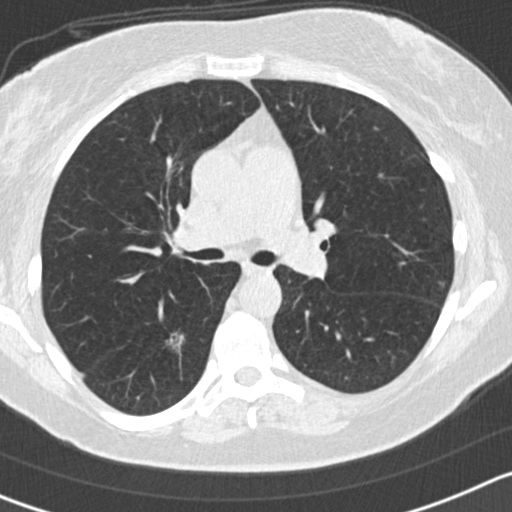
Low-dose screening chest CT, axial slice; baseline screening round; lung window (W 1500 / L -600 HU); 2 mm slice thickness; 512 × 512 image matrix. Female participant, aged 65 years at enrolment. Former smoker at enrolment.
• Expert-annotated lung lesion, bounding box [x1, y1, x2, y2] px = [144, 316, 199, 367].
• The exam's reader record, not a measurement of the box and not confirmed to be the same lesion: non-calcified nodule or mass ≥4 mm, right lower lobe, 14 × 13 mm, spiculated (stellate) margins, mixed attenuation.
• Official screen result: positive, change unspecified: nodule(s) >= 4 mm or enlarging nodule(s), mass(es), or other non-specific abnormalities suspicious for lung cancer.
• Later outcome: lung cancer diagnosed 565 days after this screen (after the second annual screen) — adenocarcinoma, NOS, right lower lobe, moderately differentiated (G2), stage IA (AJCC 6th edition), 25 mm at pathology.